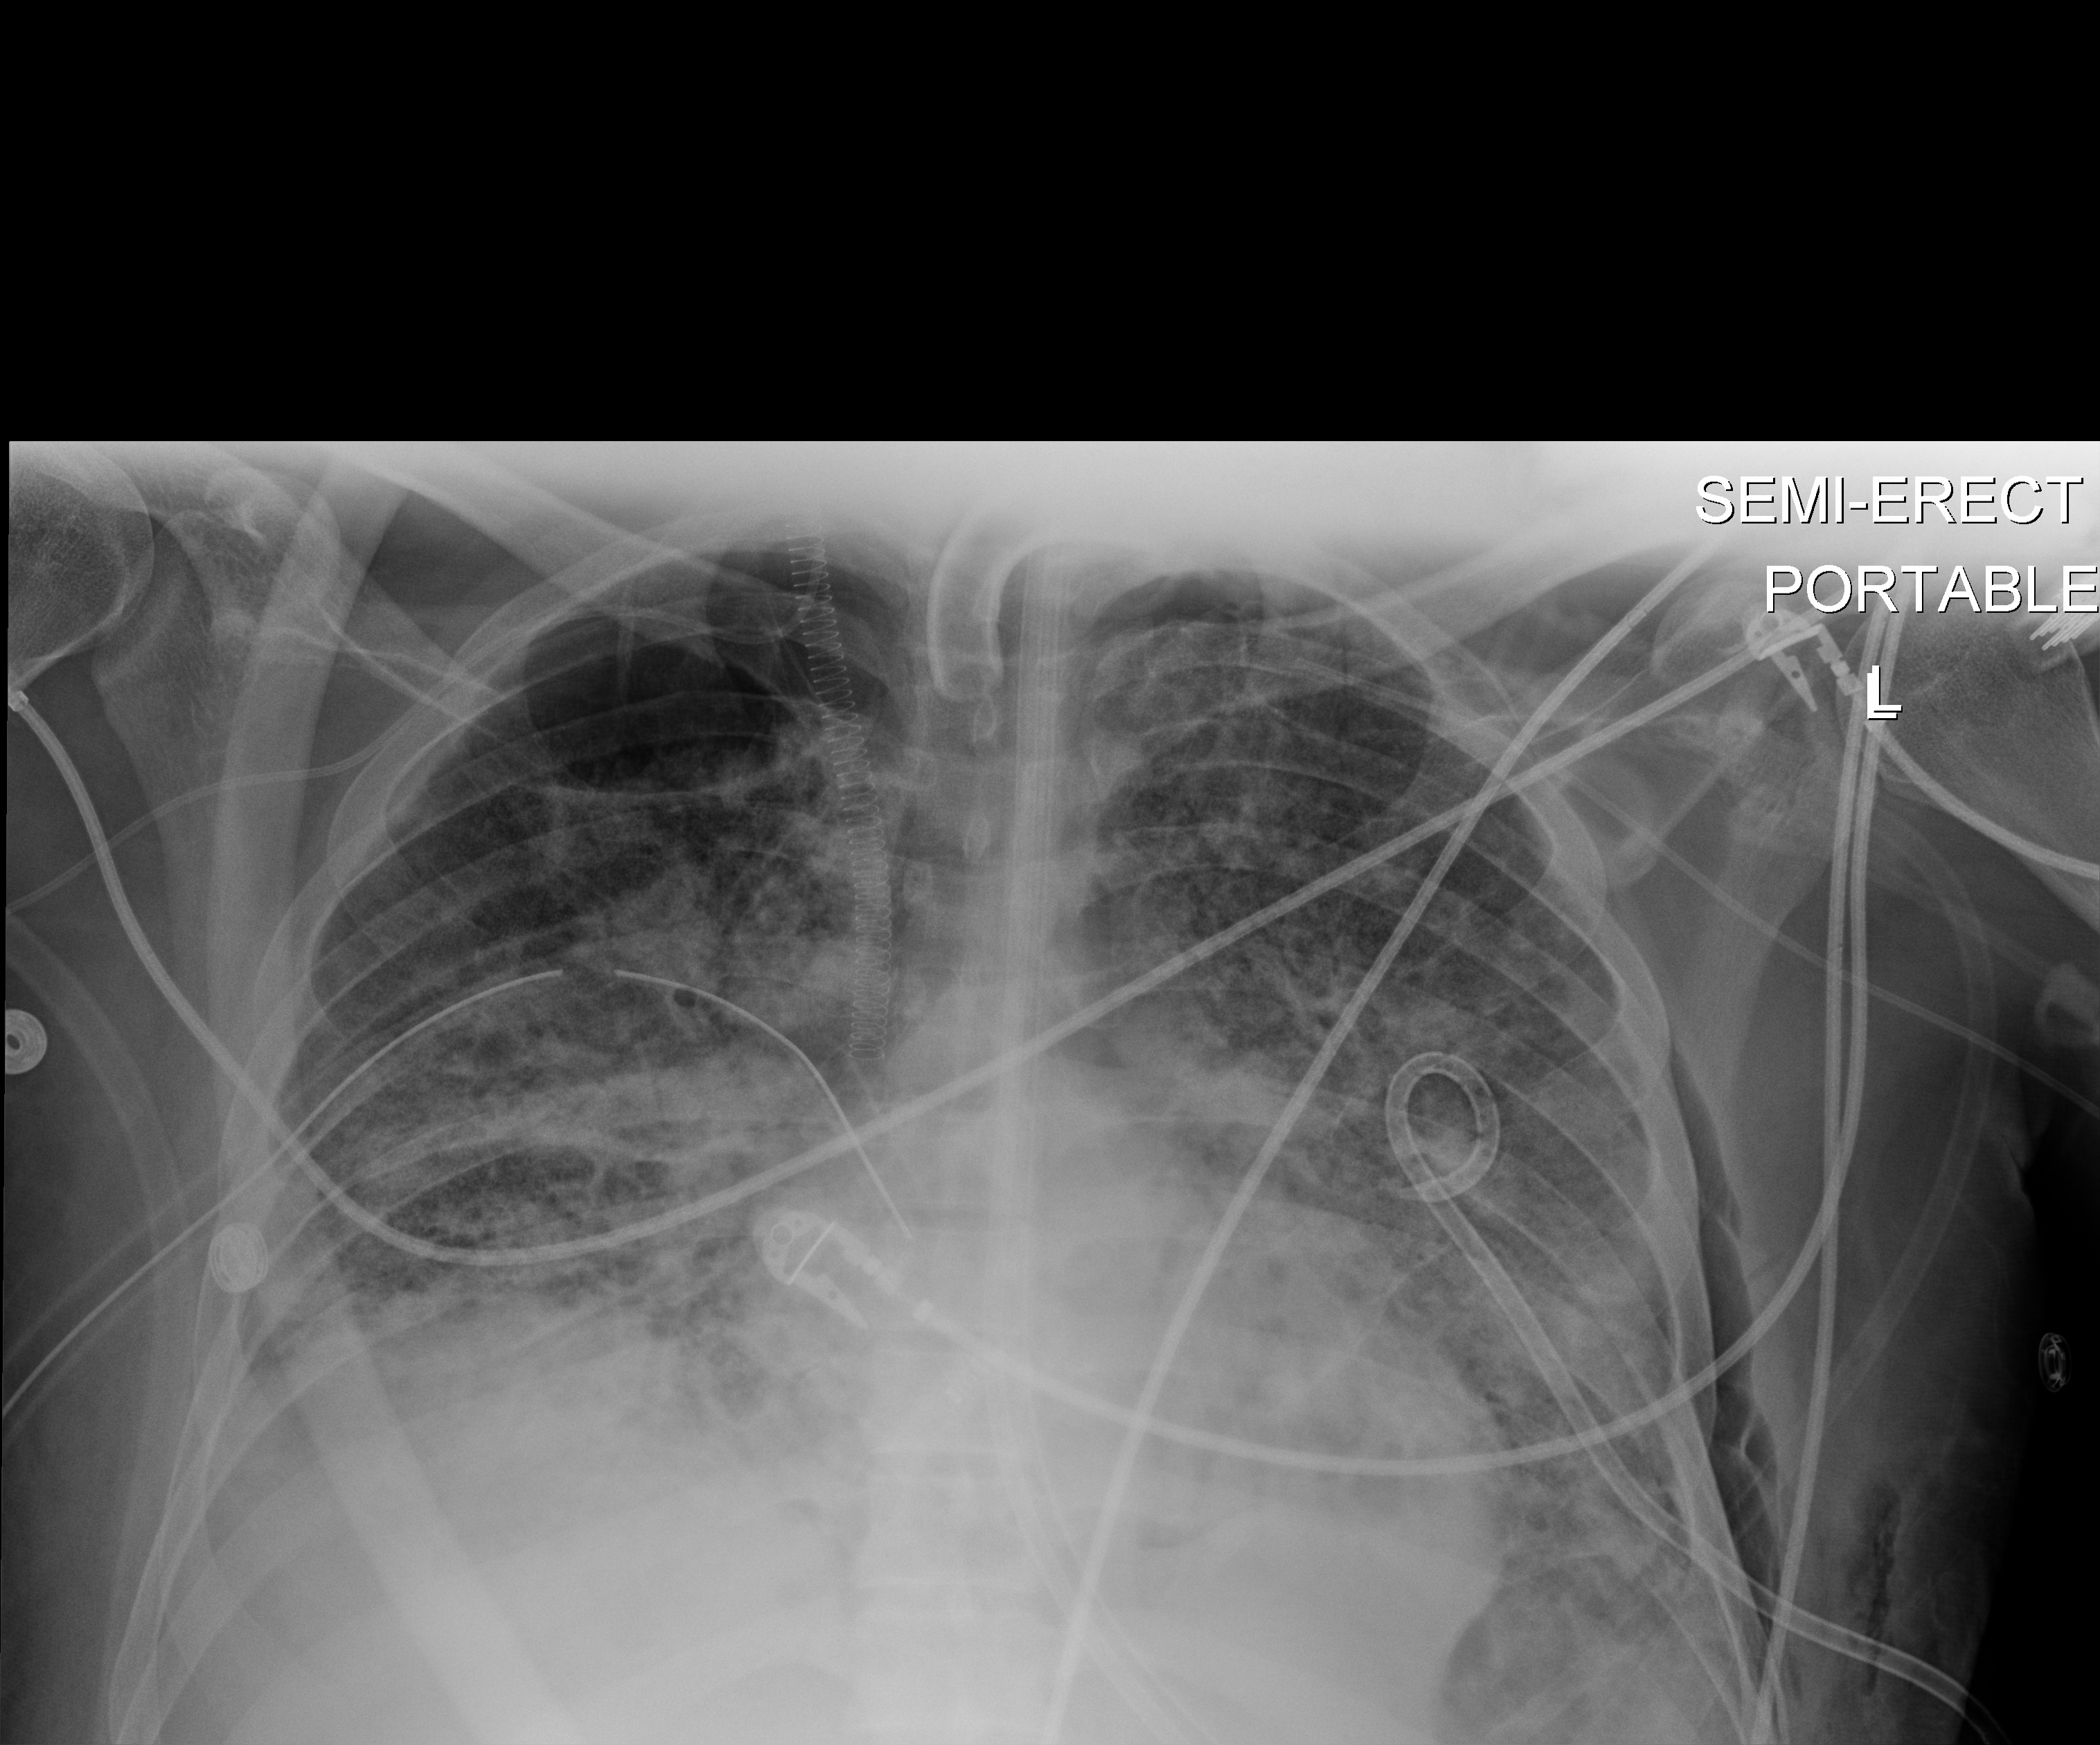
Bedside chest radiograph (digital radiography), anteroposterior (AP) projection. Patient hospitalised with COVID-19, aged 18–59 years.
Hospital-stay facts (about this admission, not read from this image; timing relative to this image not recorded): COPD (admission record): no.